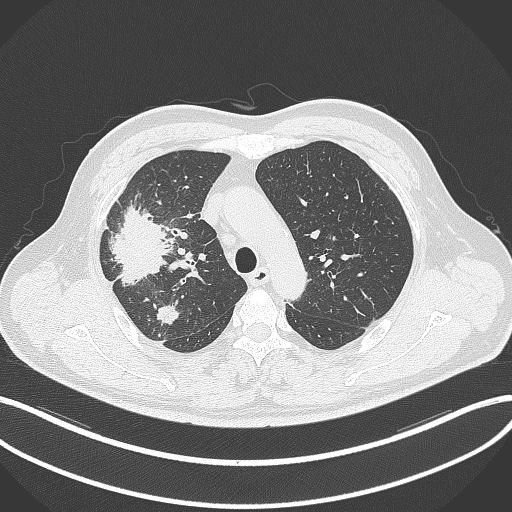
Chest CT, one axial slice. Slice 245 of 348 in the series (ordered by position). Reconstruction kernel B70f. 120 kVp. Lung window (W 1500 / L -600 HU). 1 mm slice thickness. 512 × 512 image matrix, field of view 400 × 400 mm. Patient: male, 55 years. Case-level facts recorded for this patient, not image findings: clinical TNM (as recorded): T3 N2 M1.
Structures marked on this image (bounding box drawn by a radiologist):
- lung tumour (recorded histology: adenocarcinoma): bounding box <107,201,173,289> (left, top, right, bottom; pixels)